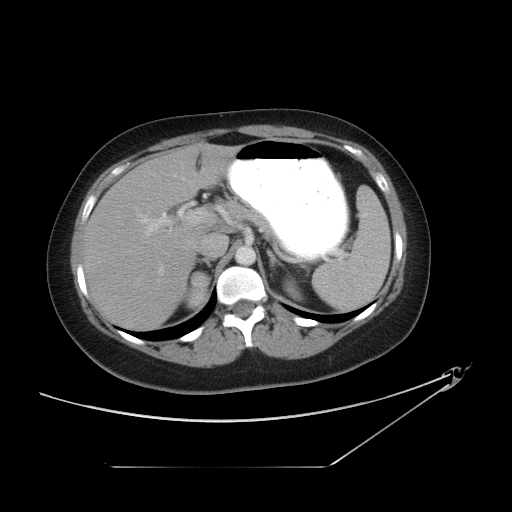
Contrast-enhanced abdominal CT, one axial slice; position 72 of 90 along the scan axis; reconstruction kernel STANDARD; 120 kVp; intravenous contrast given; soft-tissue window (W 400 / L 40 HU); 5 mm slice thickness; 512 × 512 image matrix, field of view 437 × 437 mm. Female patient, age 45 years. Case-level facts recorded for this patient, not image findings: diagnosis: adrenocortical carcinoma; tumour side: right adrenal; tumour size at pathology: 2.5 cm; Ki-67 index: 25 %; stage (as recorded): 1.
Structures marked on this image (semi-automatically segmented with operator editing):
- mass: bounding box [x1, y1, x2, y2] px = [192, 271, 209, 287]